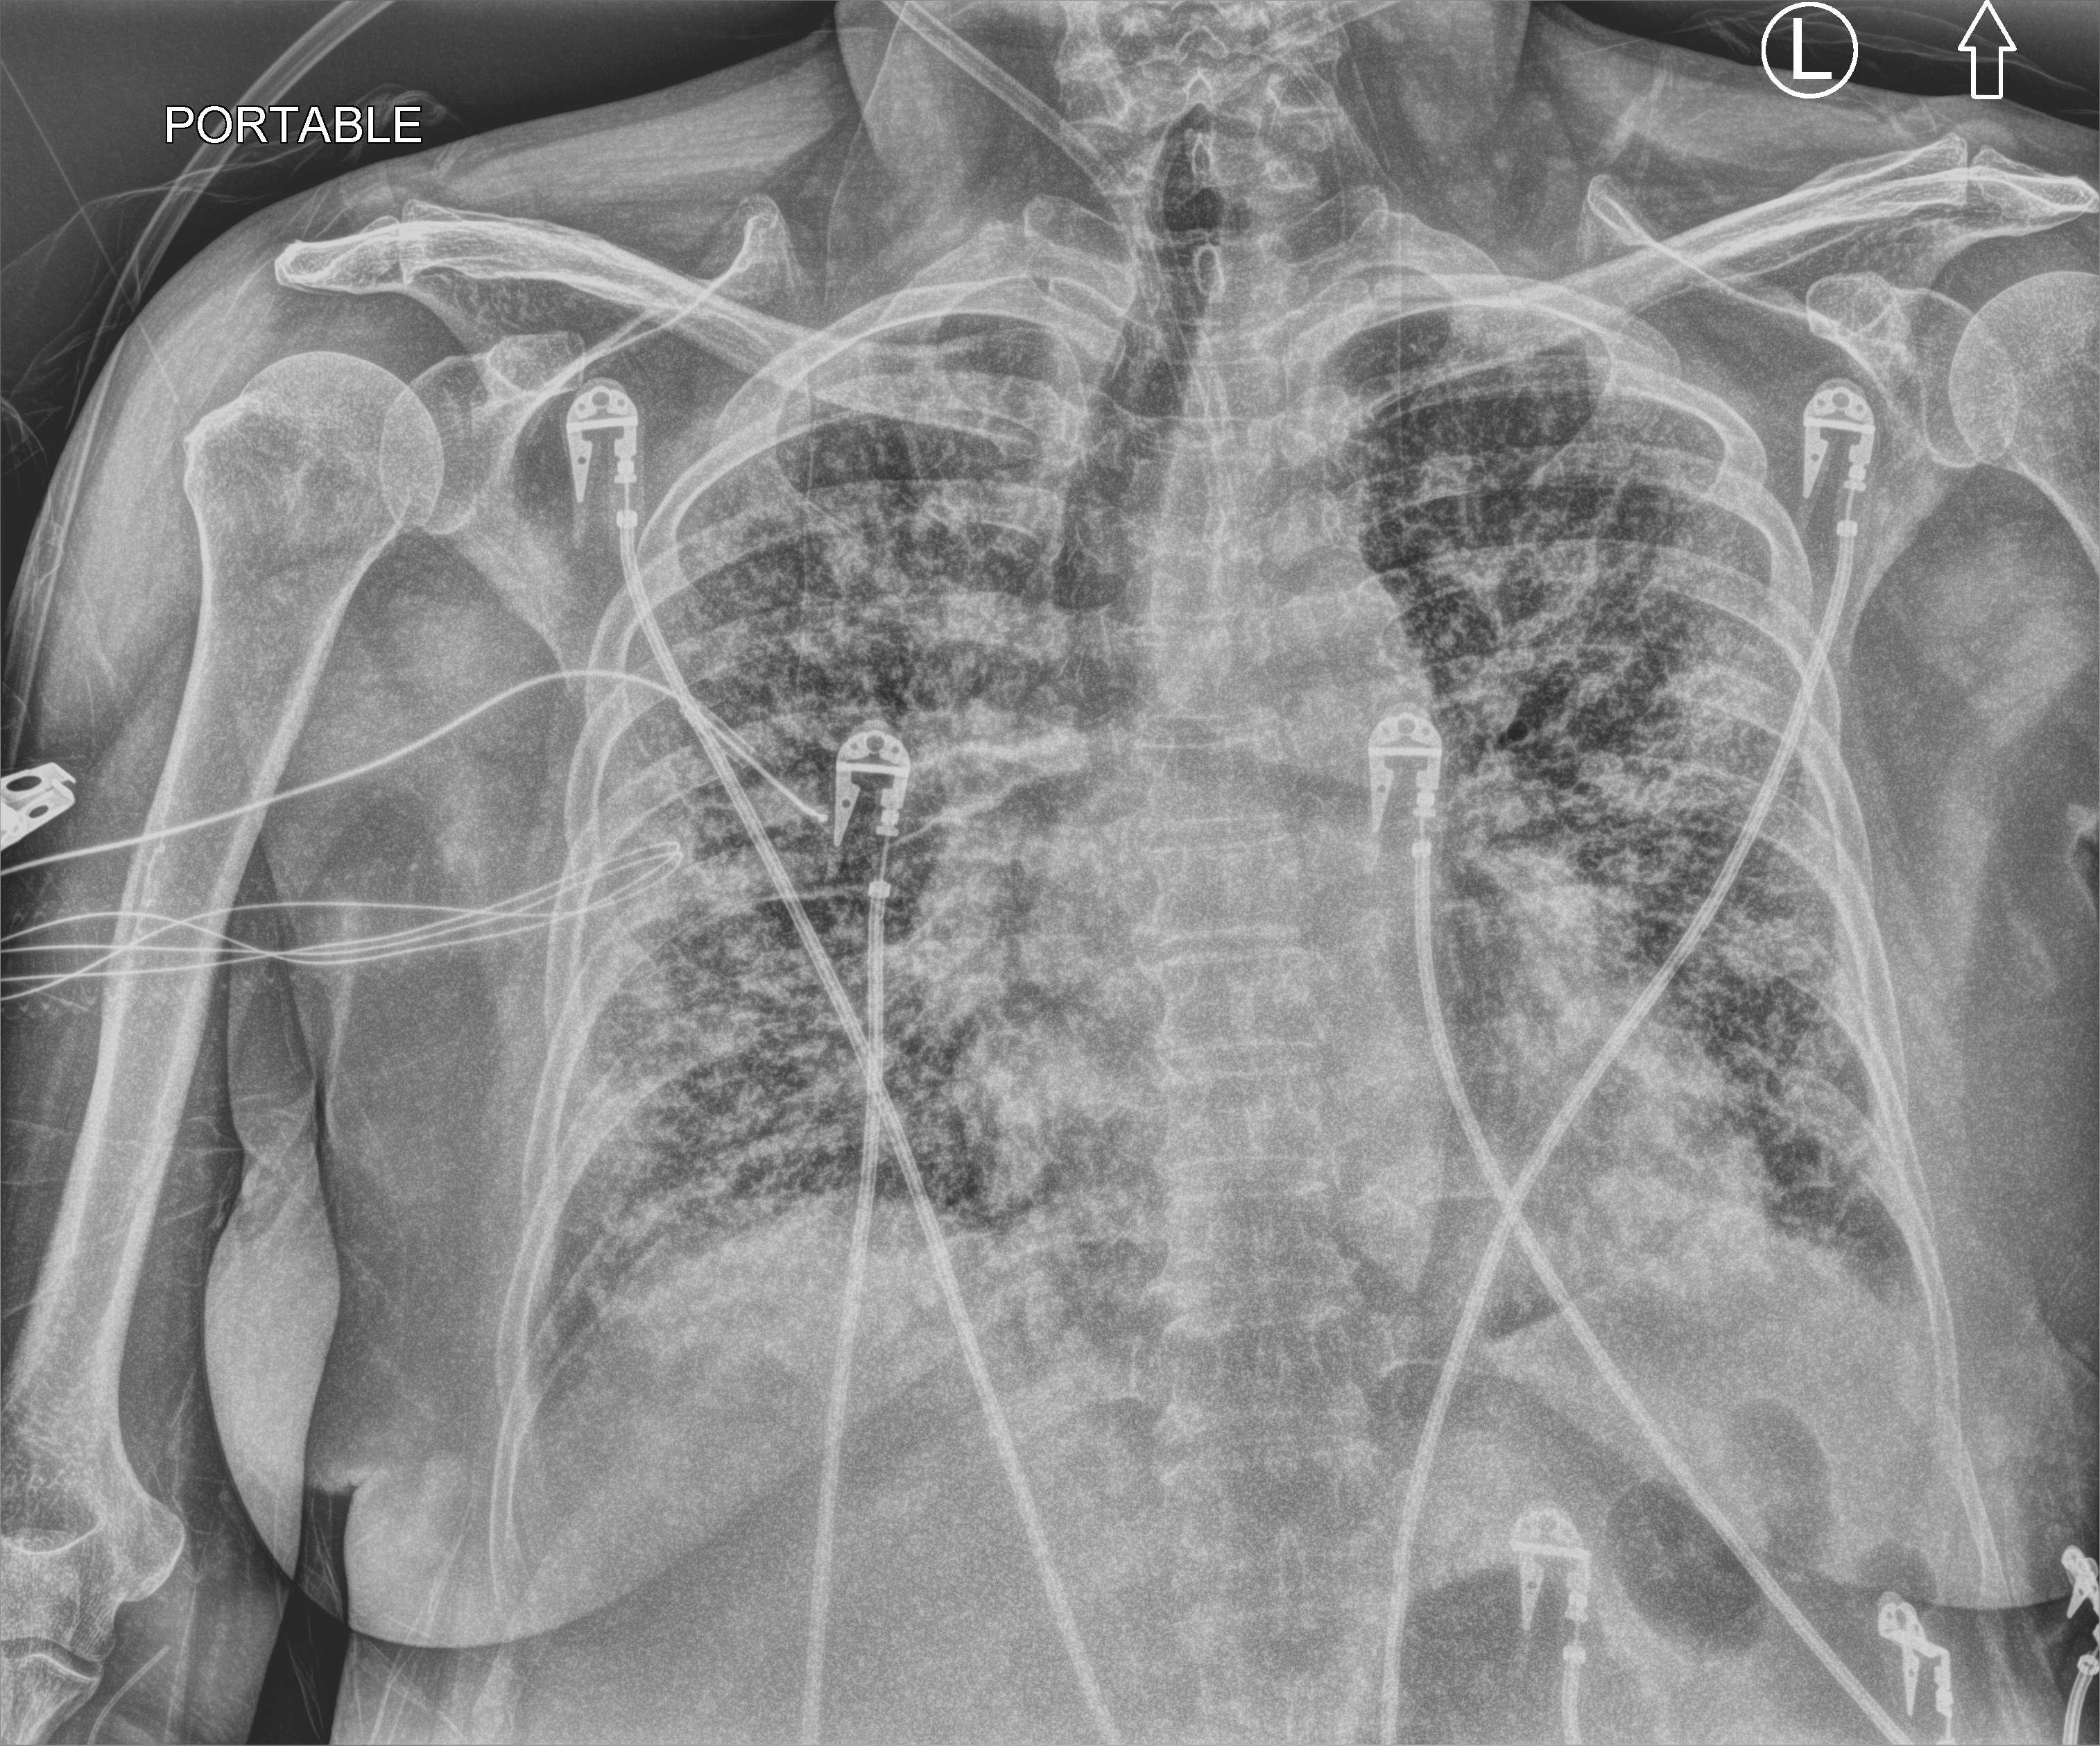
Portable chest radiograph. Patient hospitalised with COVID-19; female, aged 60–74 years.
From the hospital-stay record, not from the radiograph (when in the stay this image was taken is not recorded):
- other chronic lung disease (admission record): yes